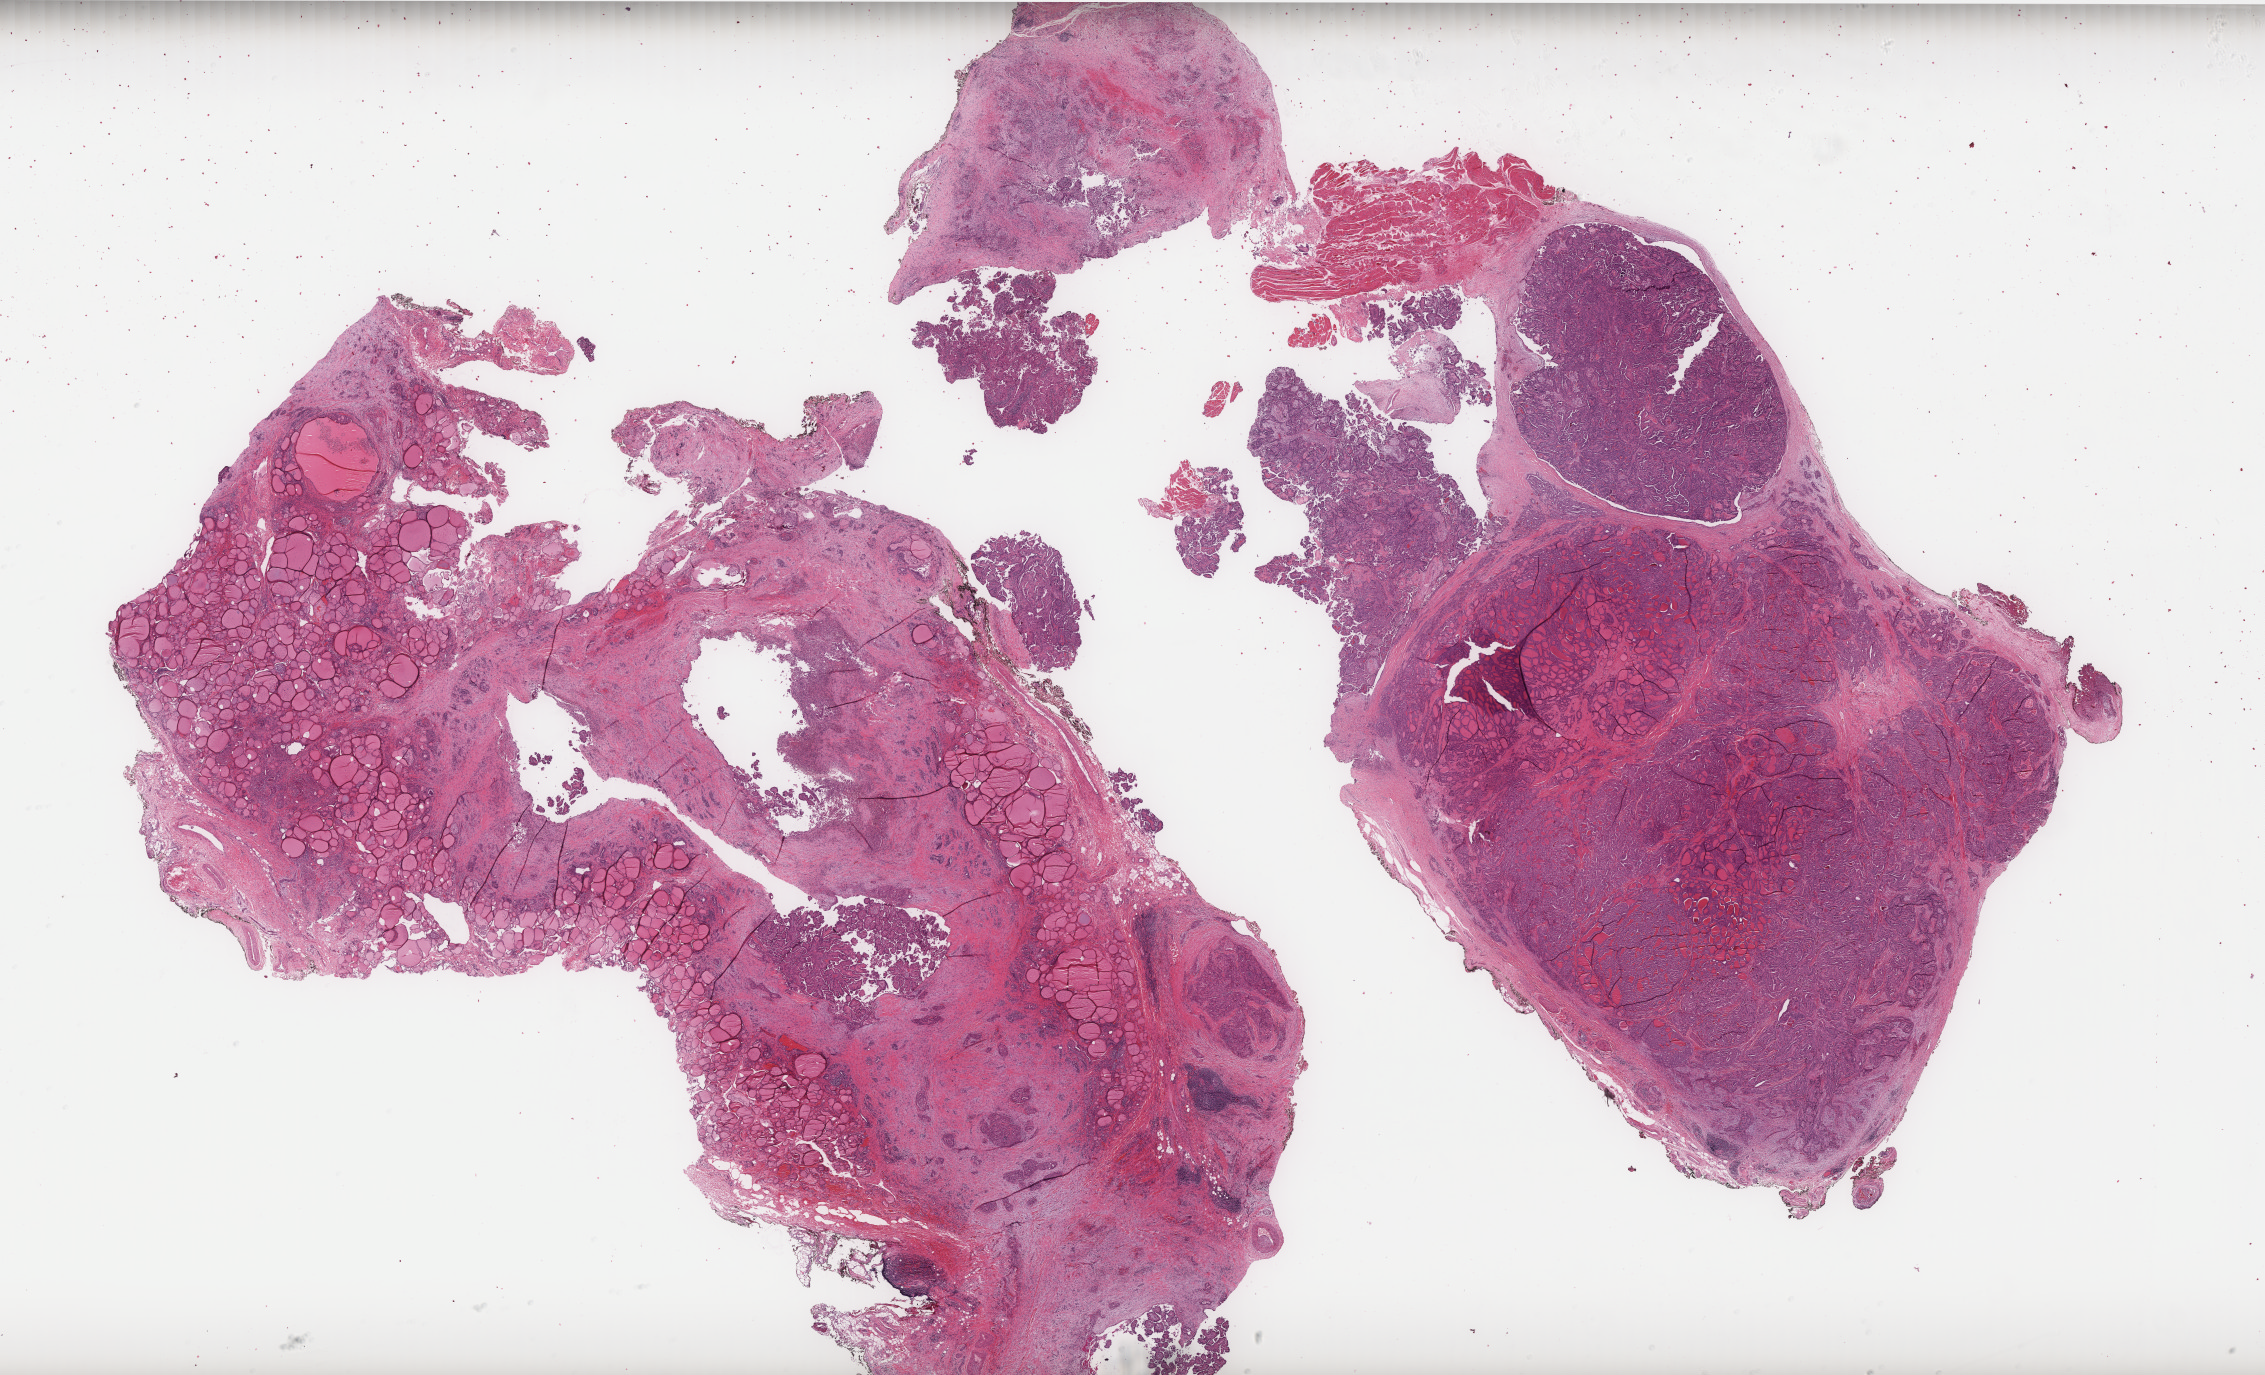
Hematoxylin and eosin (H&E) stained whole-slide image — low-resolution overview of the scanned area, about 36.3 x 22.0 mm. Formalin-fixed paraffin-embedded (FFPE) diagnostic section. Thyroid, primary tumour sample. Female, age 57 years at initial diagnosis.
* lymph nodes positive (case pathology): 0 of 6 examined
* diagnosis: Papillary carcinoma, columnar cell (thyroid gland)
* AJCC pathologic stage: III